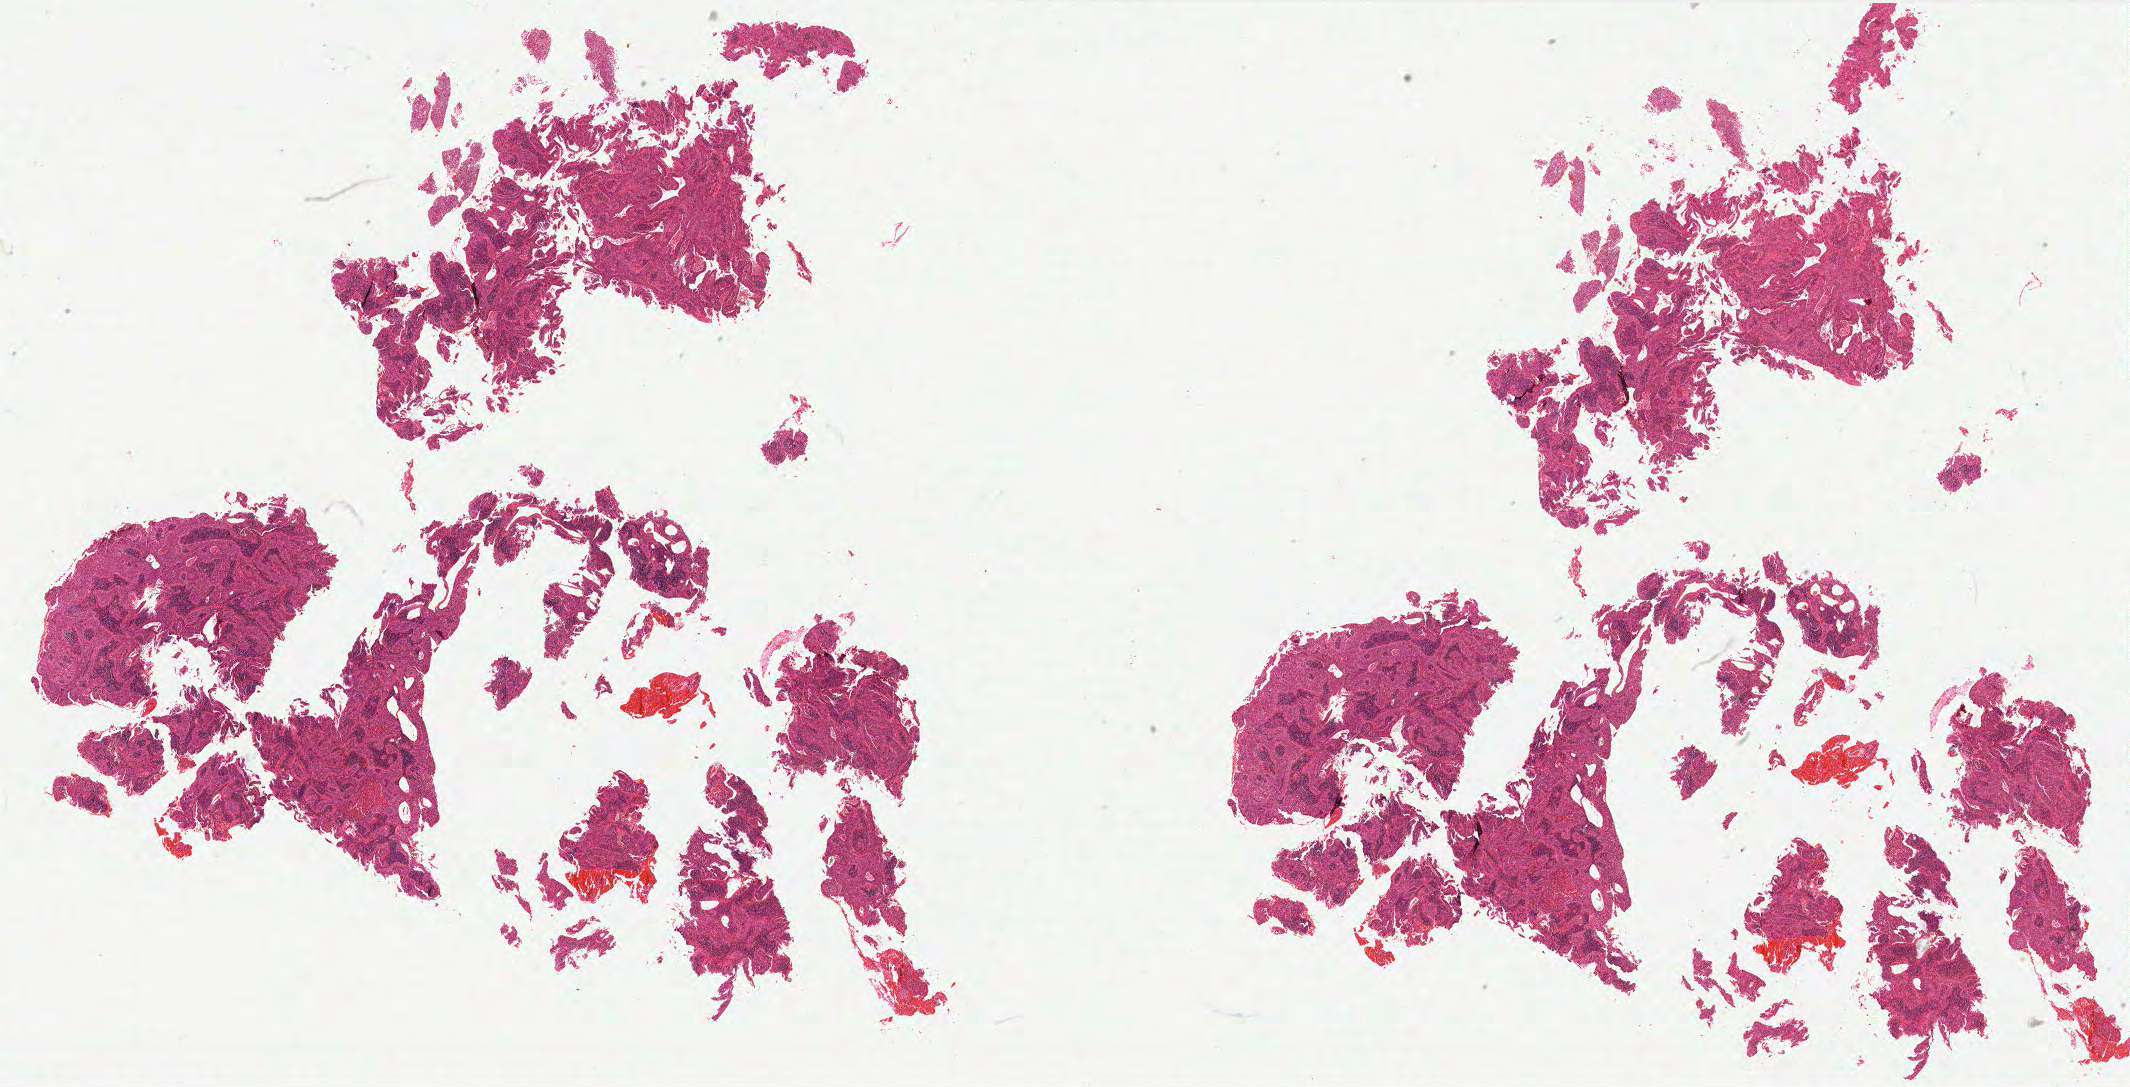
H&E whole-slide image, a low-resolution overview of the entire scanned area, about 34.1 x 17.4 mm (slide scanned at 40x), FFPE section, cervix, primary tumour sample. Female patient; age at initial diagnosis 70 years. Histologic grade: G2 (moderately differentiated).
FIGO stage: IIIB. Pathologic diagnosis: Squamous cell carcinoma, large cell, nonkeratinizing, NOS (cervix uteri).